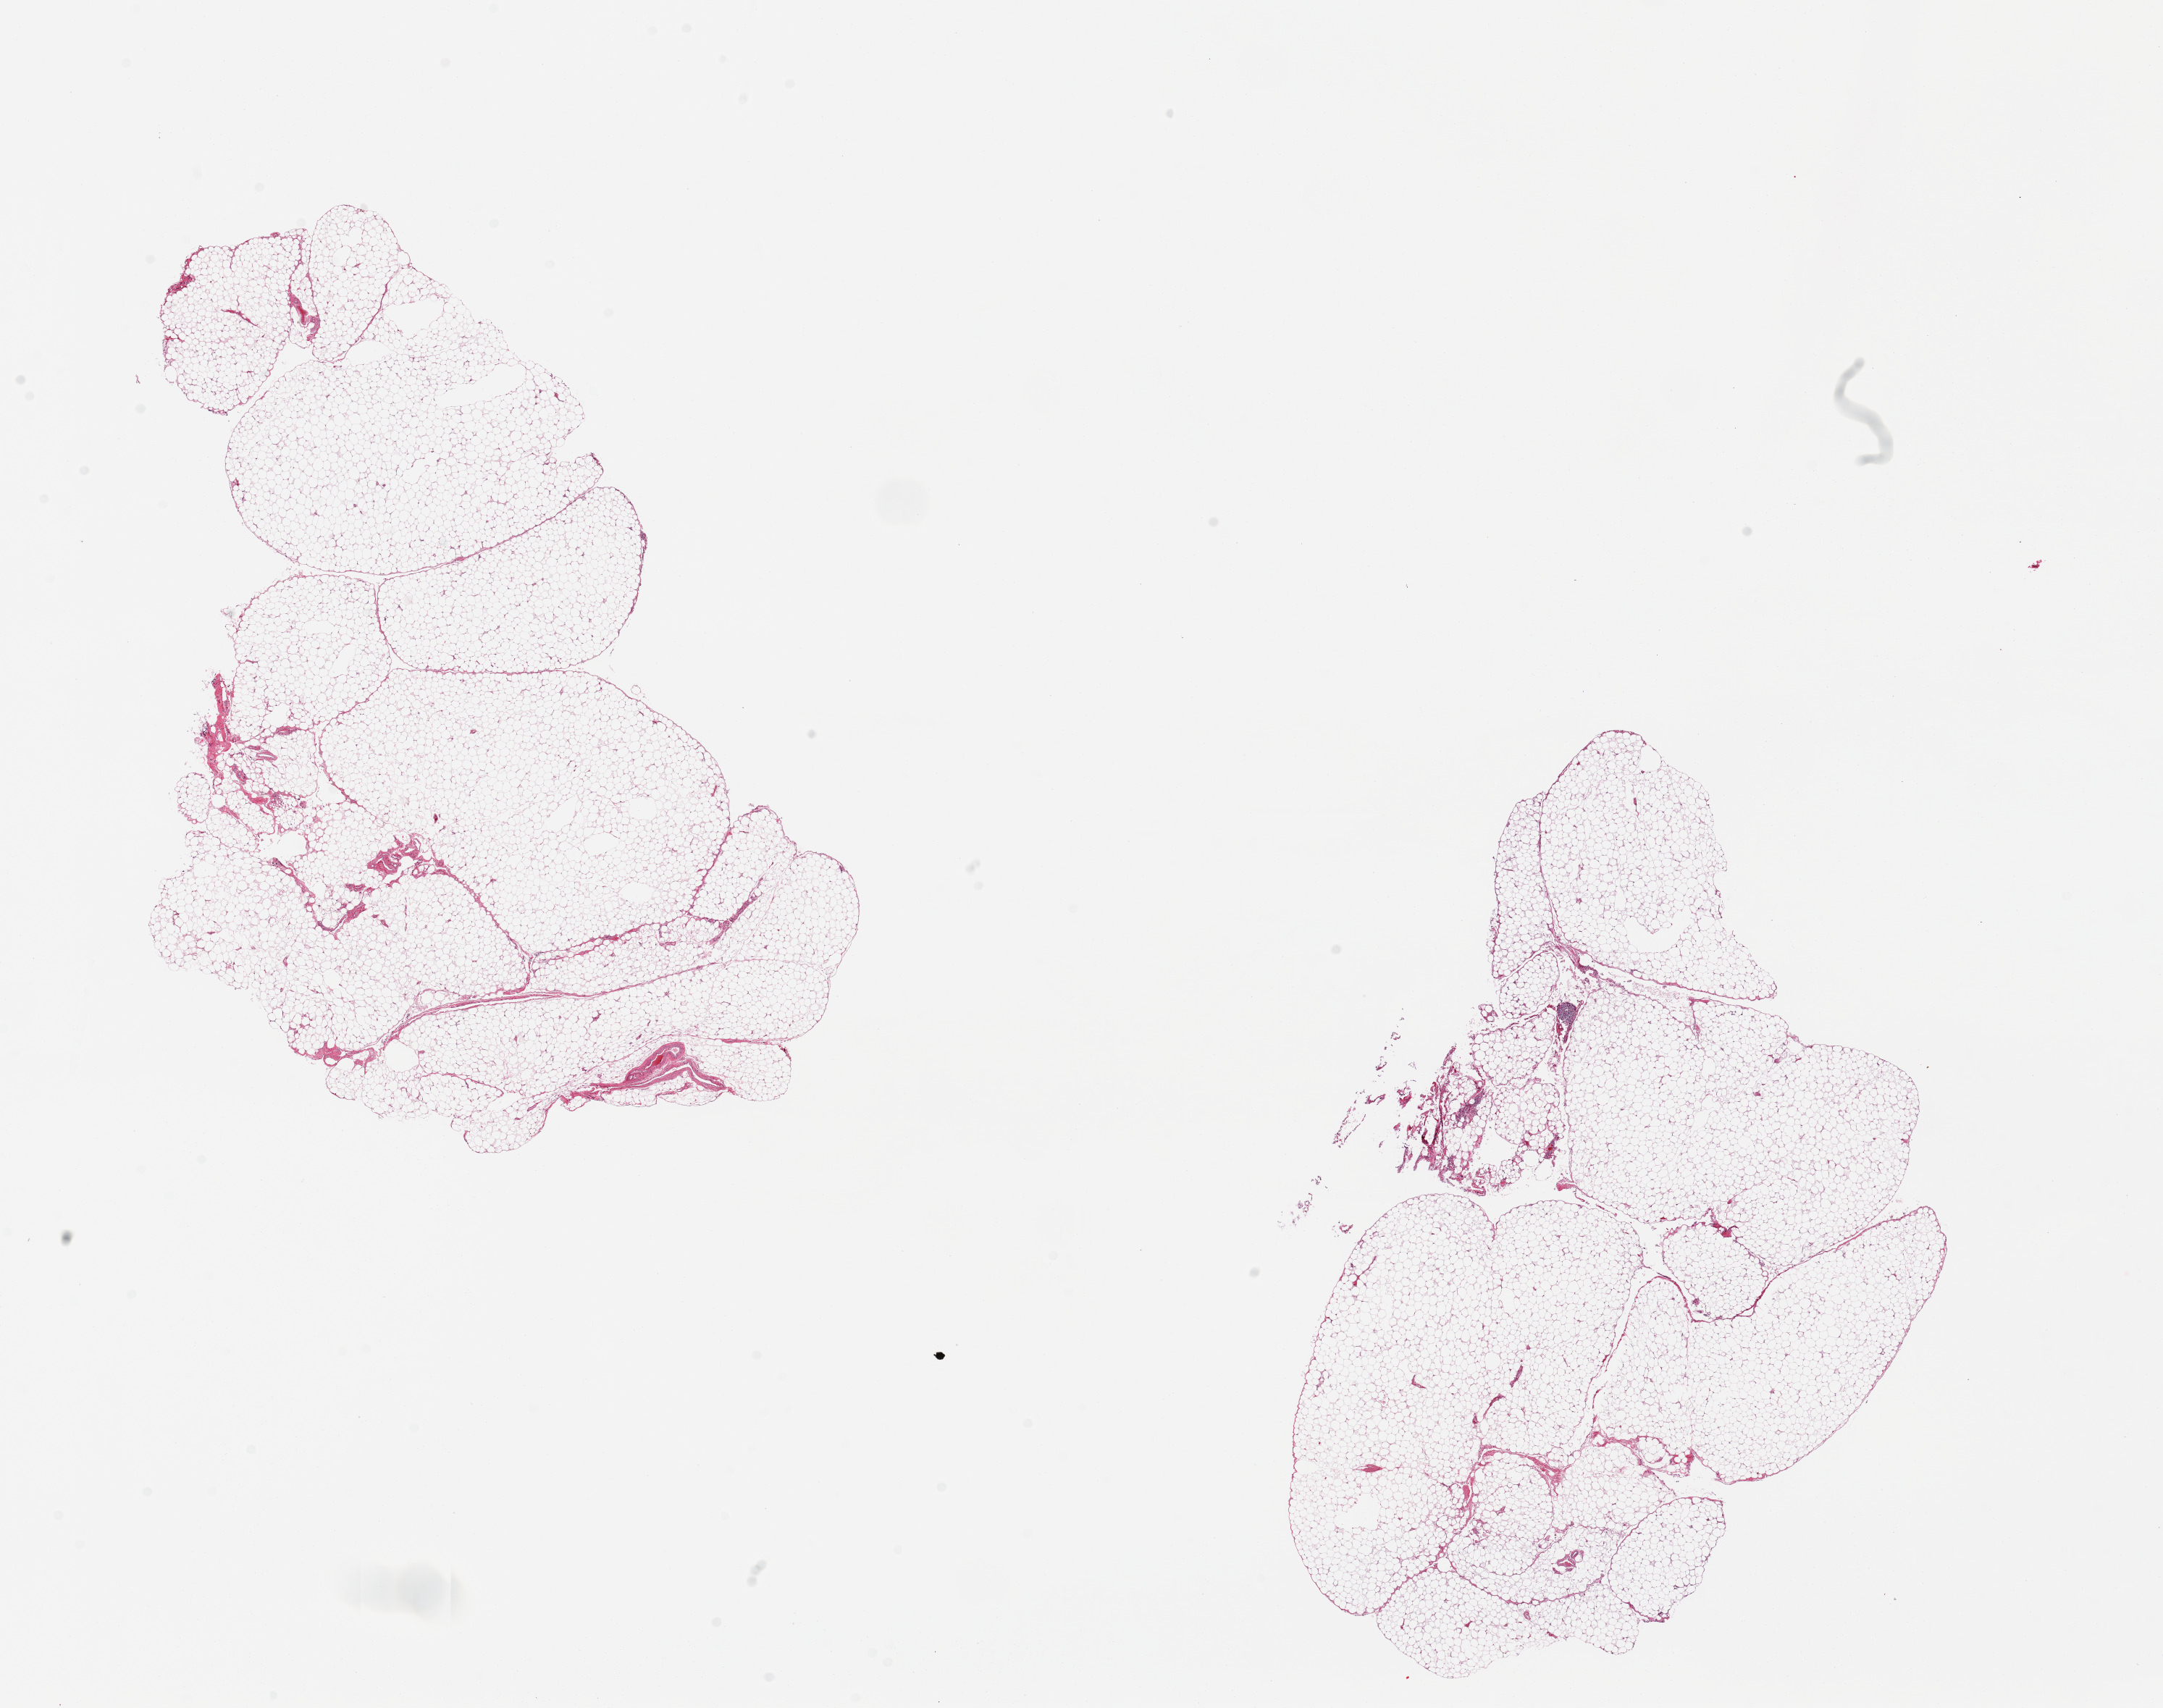
Digitized haematoxylin and eosin-stained section, brightfield, whole scanned area (about 23.6 x 18.7 mm, from a 20x scan) shown as a low-resolution overview. PAXgene-fixed, paraffin-embedded tissue. Sampled site (target tissue): omentum. Tissue donor sample.
Review note (as recorded): 2 pieces. 11x7 & 10x7mm.